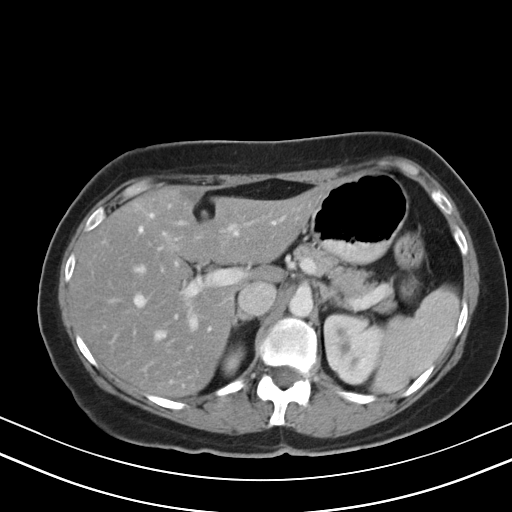
Contrast-enhanced abdominal CT, one axial slice; position 30 of 47 along the scan axis; reconstruction kernel B40s; 130 kVp; intravenous contrast given; soft-tissue window (W 400 / L 40 HU); 5 mm slice thickness; 512 × 512 image matrix. Female patient. From the clinical record (not read from this slice): diagnosis: colorectal cancer liver metastases, imaged before liver resection; multiple liver metastases: no; largest metastasis: 3.5 cm; disease in both lobes: no.
Annotated regions visible in this slice (manually delineated by an expert):
- hepatic veins: box from (x=134, y=214) to (x=282, y=339) px
- liver: (x=71, y=183)–(x=336, y=396)
- planned liver remnant (the part of the liver to remain after resection): (x=71, y=183)–(x=336, y=396)
- portal vein (with intrahepatic branches): (x=138, y=227)–(x=241, y=330)